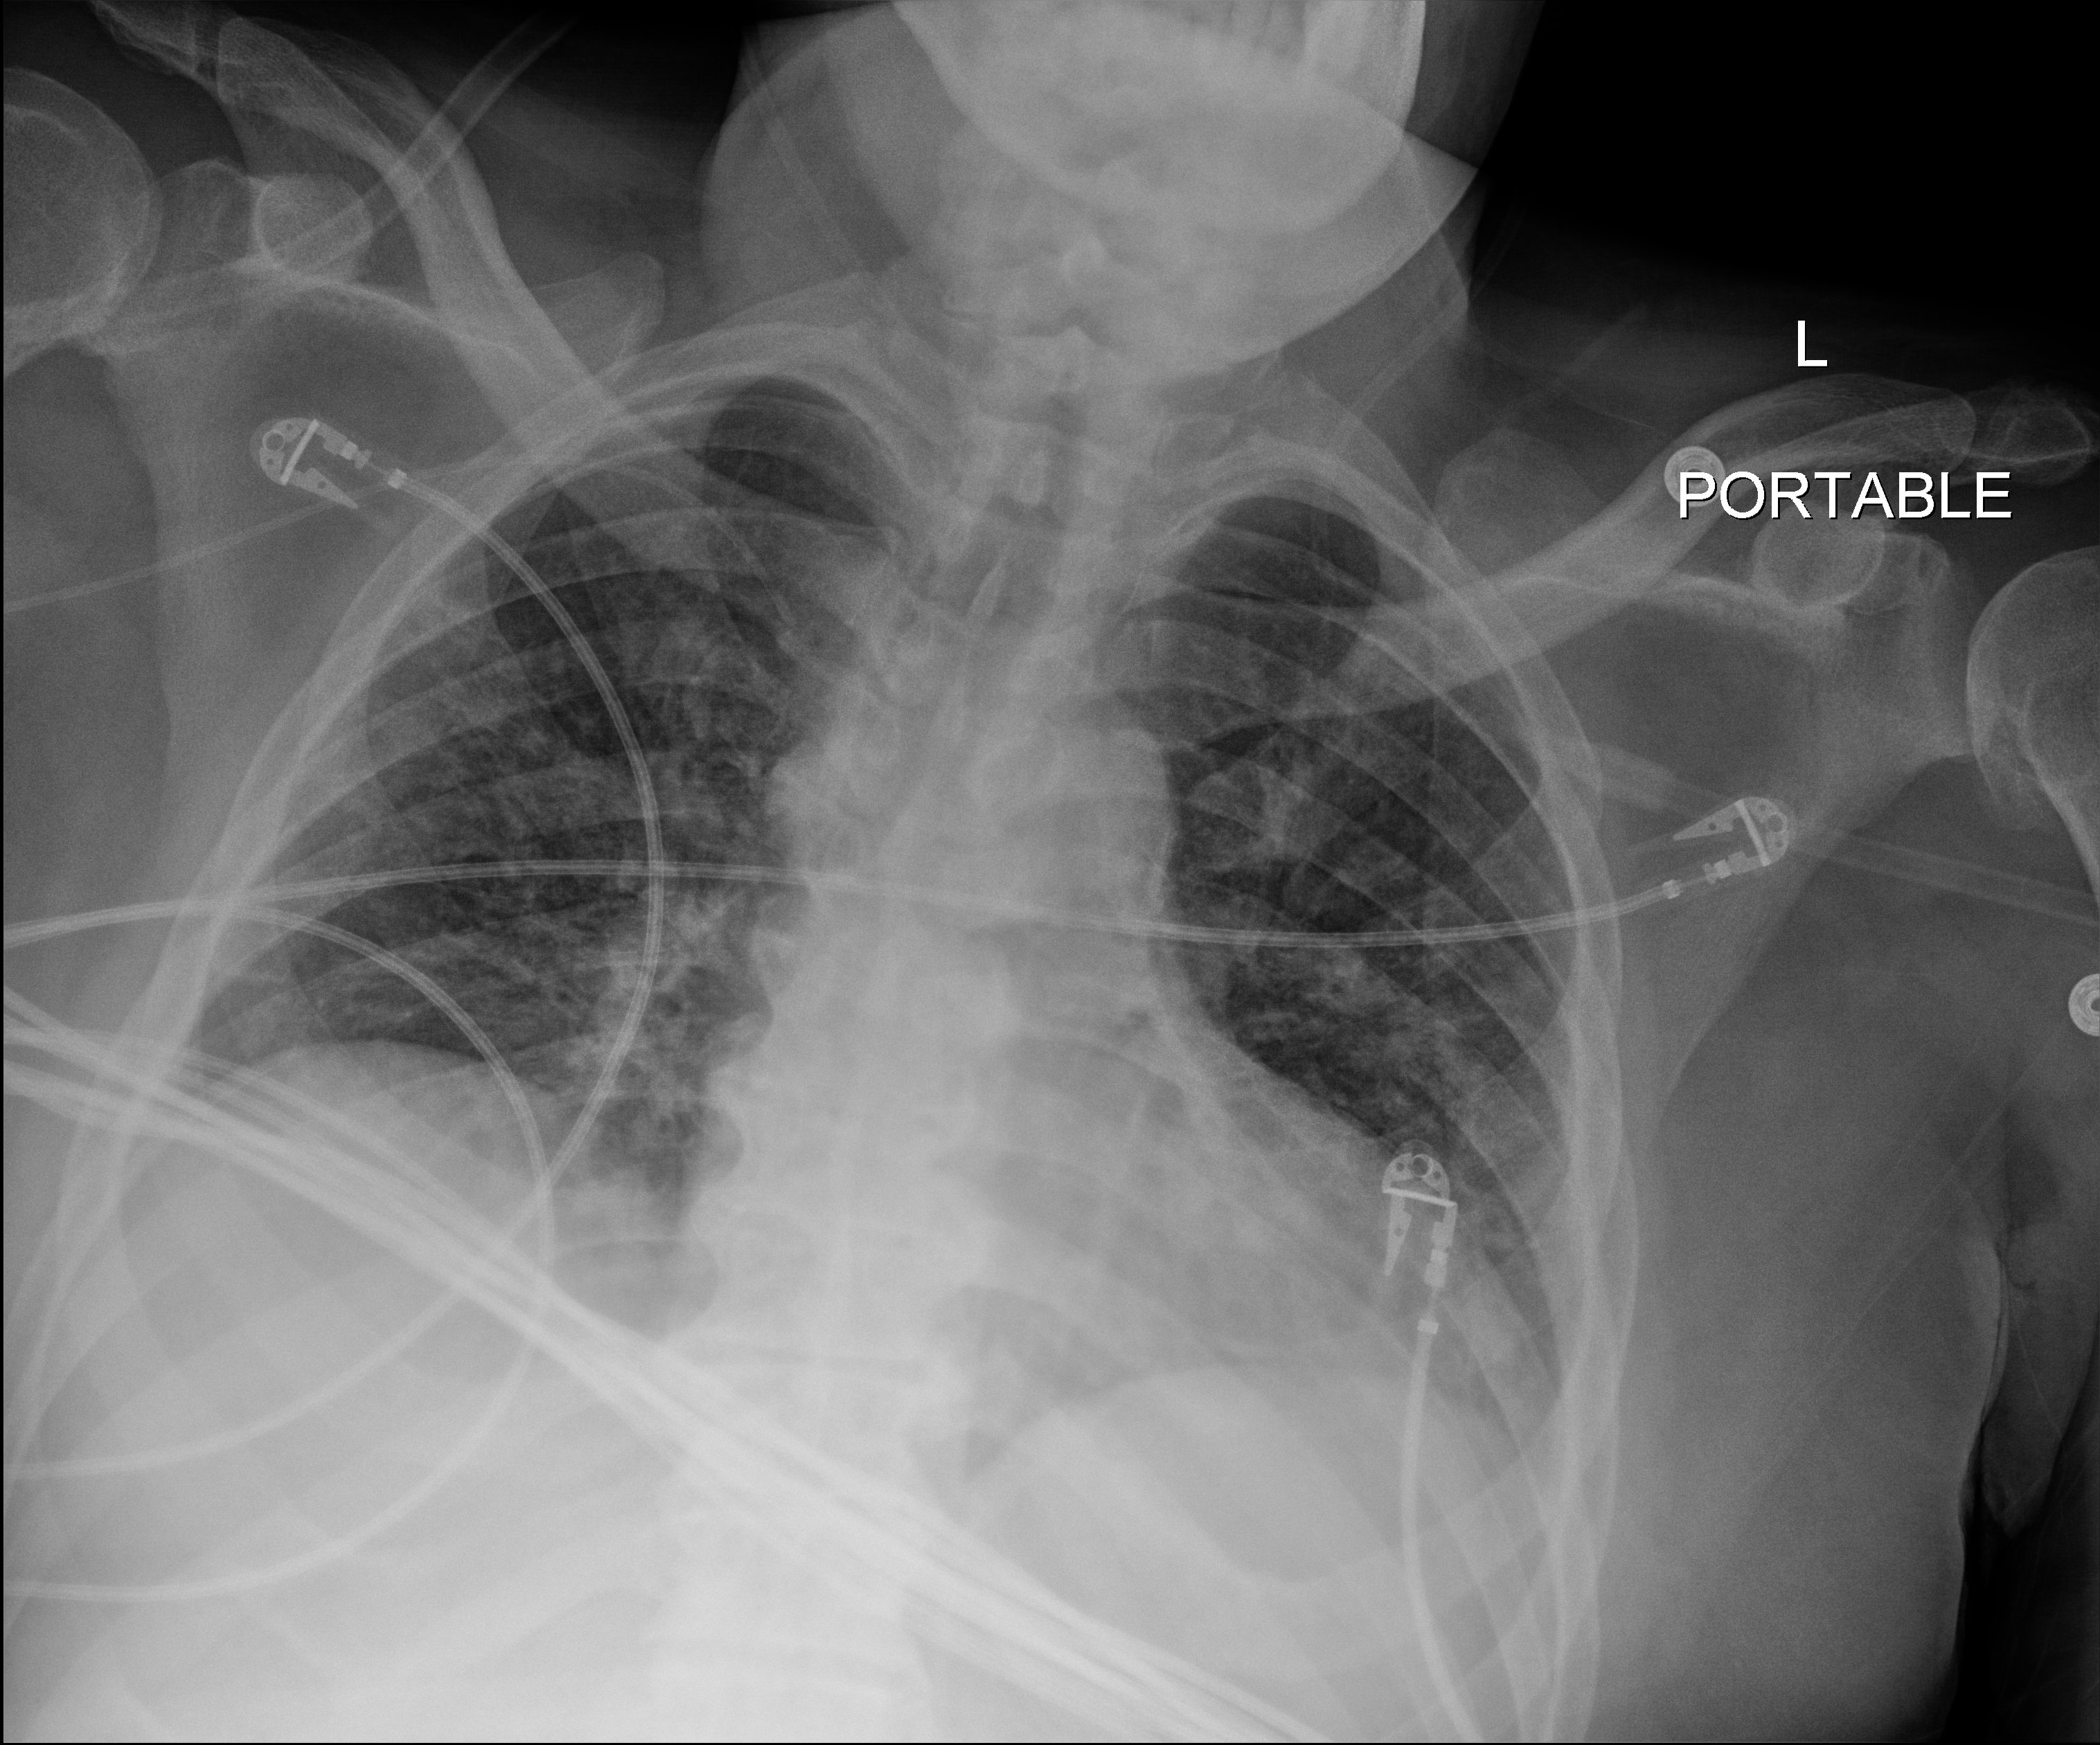
Chest X-ray (portable); anteroposterior (AP) projection. Patient hospitalised with COVID-19; male, aged 18–59 years.
Hospital-stay facts (about this admission, not read from this image; timing relative to this image not recorded):
- mechanically ventilated during this hospital stay: yes
- admitted to intensive care during this hospital stay: yes